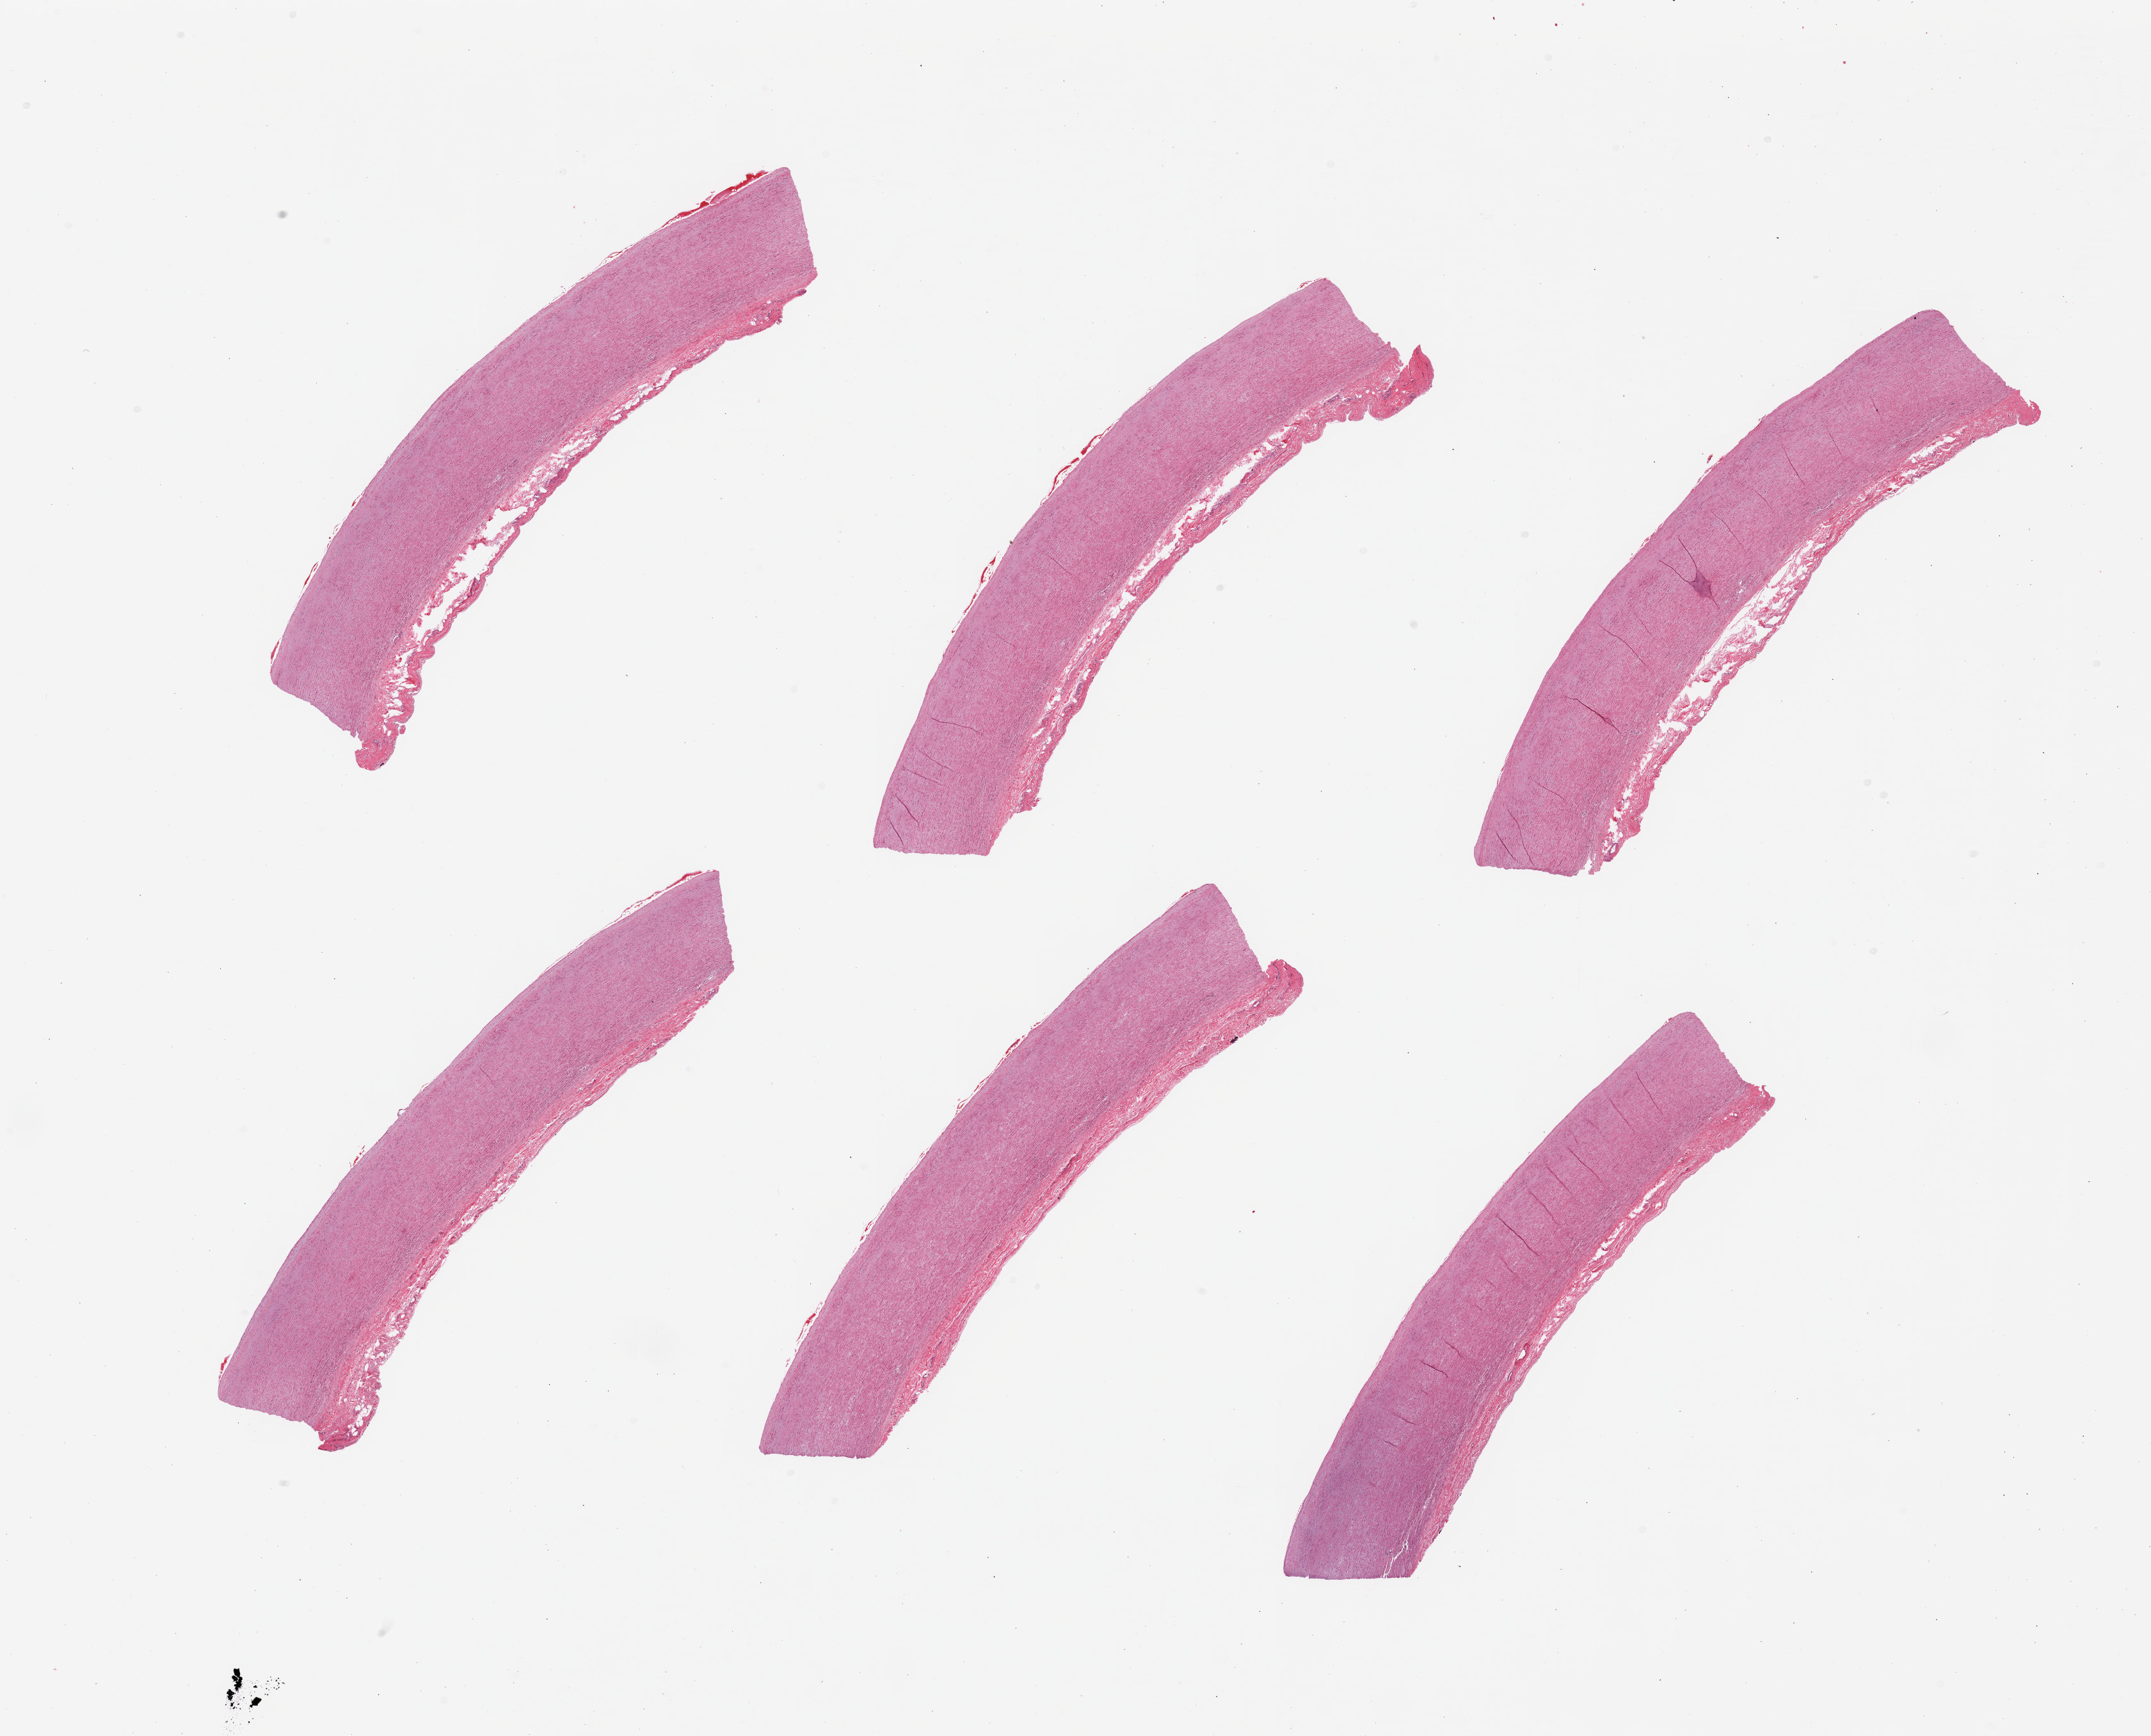
Hematoxylin and eosin (H&E) whole-slide image, a low-resolution overview of the entire scanned area, about 26.6 x 21.5 mm. PAXgene-fixed, paraffin-embedded tissue. Target tissue: aorta. Donor tissue sample. Donor: female.
Reviewer comment on this tissue sample: 6 pieces; well dissected; minimal intimal plaque.